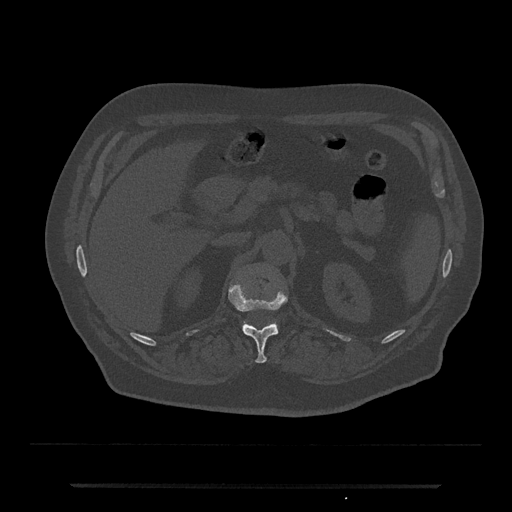
CT including the spine, one axial slice. Slice 579 of 797 in the series (ordered by position). 120 kVp. Bone window (W 1800 / L 400 HU). 0.5 mm slice thickness. 512 × 512 image matrix. Patient: male, 80 years. Case-level facts recorded for this patient, not image findings: primary cancer: prostate; vertebrae with lytic lesions (as recorded): L1, T11.
Outlined on this slice (semi-automatic segmentation, software-assisted and operator-edited):
- L1 vertebra: bounding box <242,321,278,328> (left, top, right, bottom; pixels)
- T12 vertebra: <229,284,287,363>